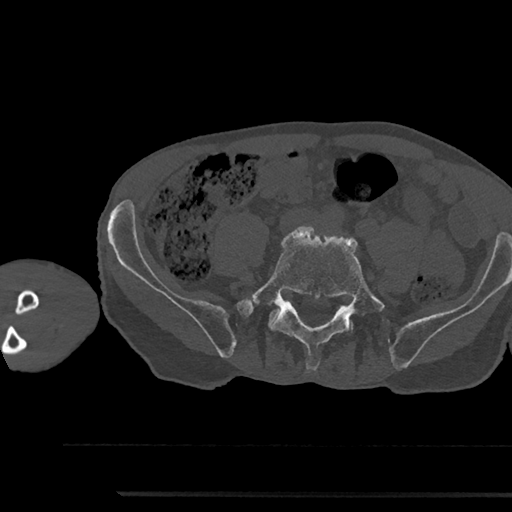
CT including the spine, one axial slice. Slice 346 of 797 in the series (ordered by position). Reconstruction kernel Br40s/3. 120 kVp. Bone window (W 1800 / L 400 HU). 512 × 512 image matrix, field of view 367 × 367 mm. Male patient, age 79 years. From the clinical record (not read from this slice): primary cancer: prostate.
Structures marked on this image (semi-automatically segmented with operator editing):
- L5 vertebra: bounding box <245,226,385,370> (left, top, right, bottom; pixels)